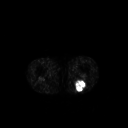
FDG PET of an extremity soft-tissue mass (from a PET/CT study), one axial slice; slice 198 of 267 in the series (ordered by position); 128 × 128 image matrix, field of view 500 × 500 mm. Patient: male, 54 years. Case-level facts recorded for this patient, not image findings: histological type: synovial sarcoma; site of the primary tumour: left poplietal fossa.
Structures marked on this image (expert contour drawn on MRI and transferred to this co-registered scan by the dataset authors):
- gross tumour volume (mass): bounding box (x1, y1, x2, y2) in pixels: (74, 80, 86, 91)